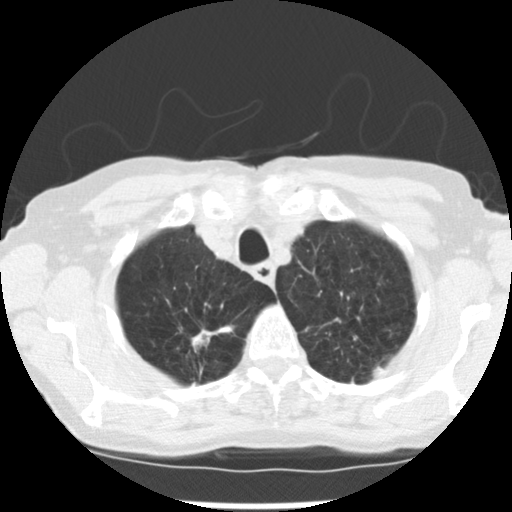
Low-dose screening chest CT, axial slice; first (baseline) screen; lung window (W 1500 / L -600 HU); slice 33 of 265 in the series. Female participant, aged 72 years at enrolment.
Lesion marked by an expert reader, bounding box (x1, y1, x2, y2) in pixels: (178, 313, 232, 354). The screening reader recorded 3 non-calcified nodules or masses ≥4 mm on this exam (right upper lobe, left upper lobe, left lower lobe); which of them this box marks is not recorded. Official screen result: positive, change unspecified: nodule(s) >= 4 mm or enlarging nodule(s), mass(es), or other non-specific abnormalities suspicious for lung cancer. Lung cancer was diagnosed 50 days after this screen: adenocarcinoma, NOS, right upper lobe, moderately differentiated (G2), stage IB (AJCC 6th edition), 22 mm at pathology.